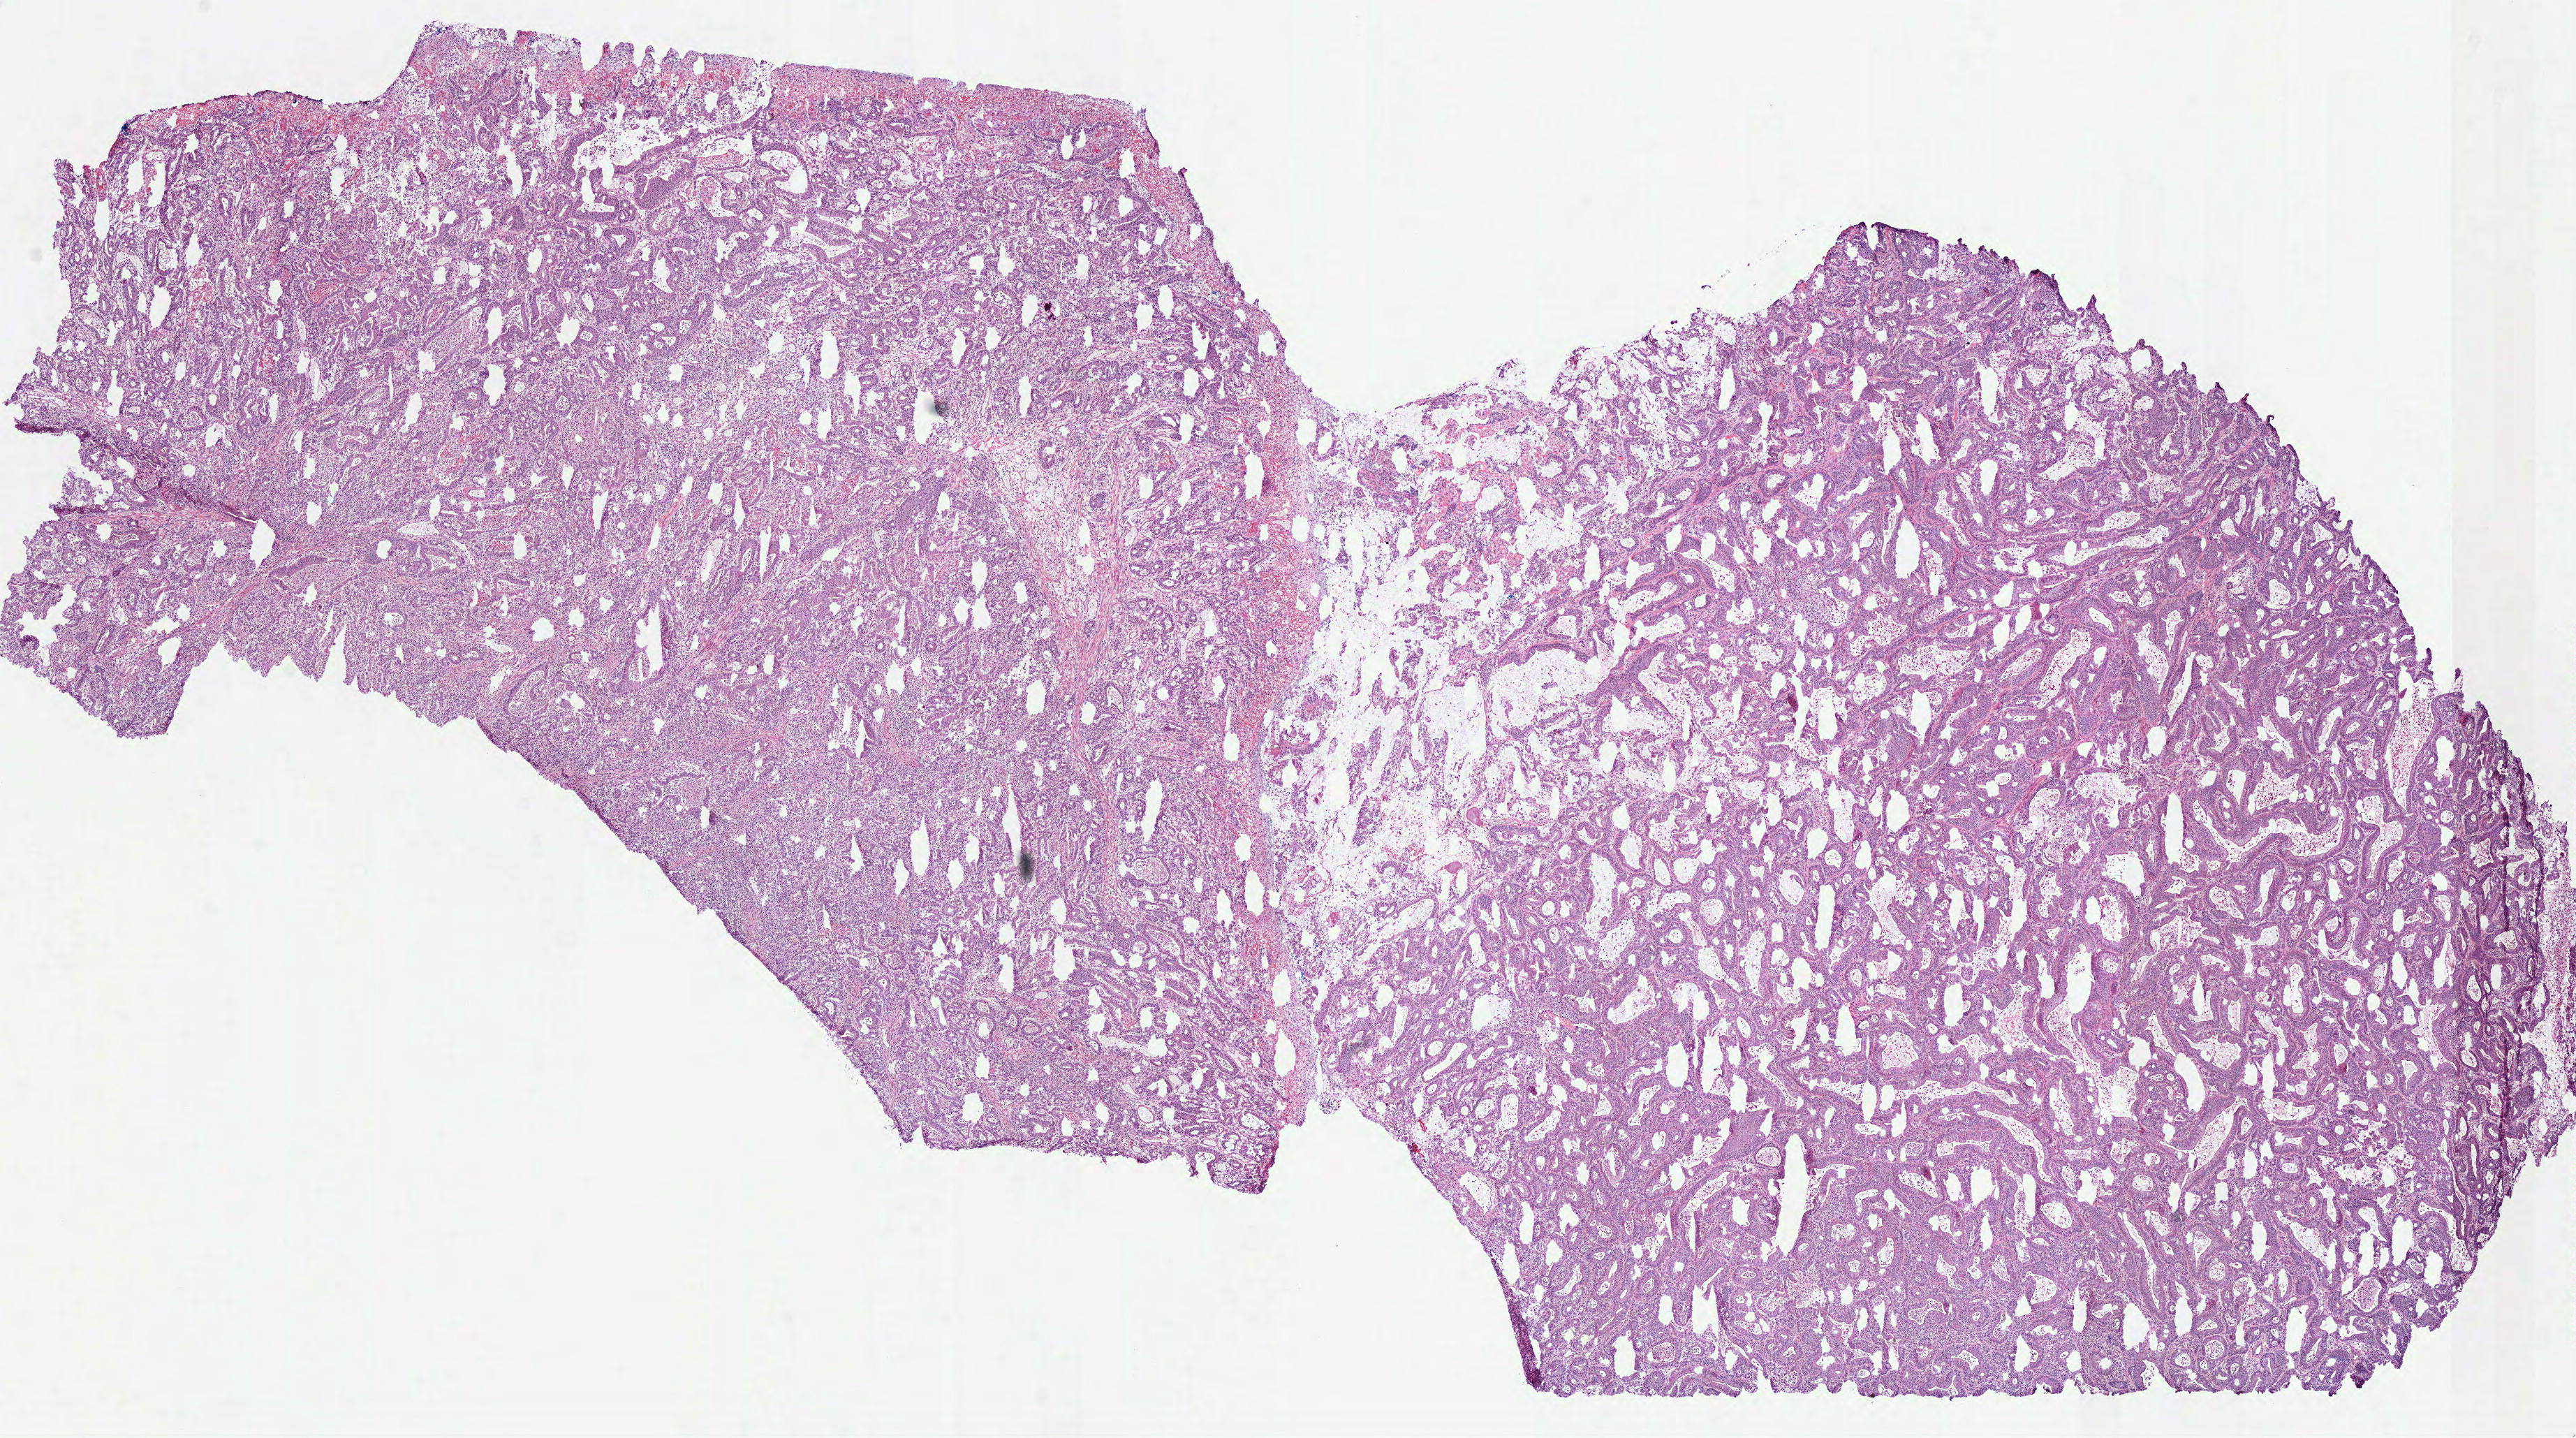
Digitized H&E tissue section (whole slide), whole scanned area (about 14.5 x 8.1 mm, from a 40x scan) shown as a low-resolution overview, frozen section from the bottom of the tissue portion, primary tumour sample from the stomach. Male patient; age at initial diagnosis 79 years. Histologic grade: G3 (poorly differentiated). Composition of this section per pathologist review: tumour cells 80%, tumour nuclei 80%, normal cells 0%, stromal cells 15%, necrosis 5%. Inflammatory infiltration, as recorded: lymphocyte infiltration 3%, neutrophil infiltration 2%.
* diagnosis: Adenocarcinoma, intestinal type (cardia, NOS)
* AJCC pathologic stage: IB